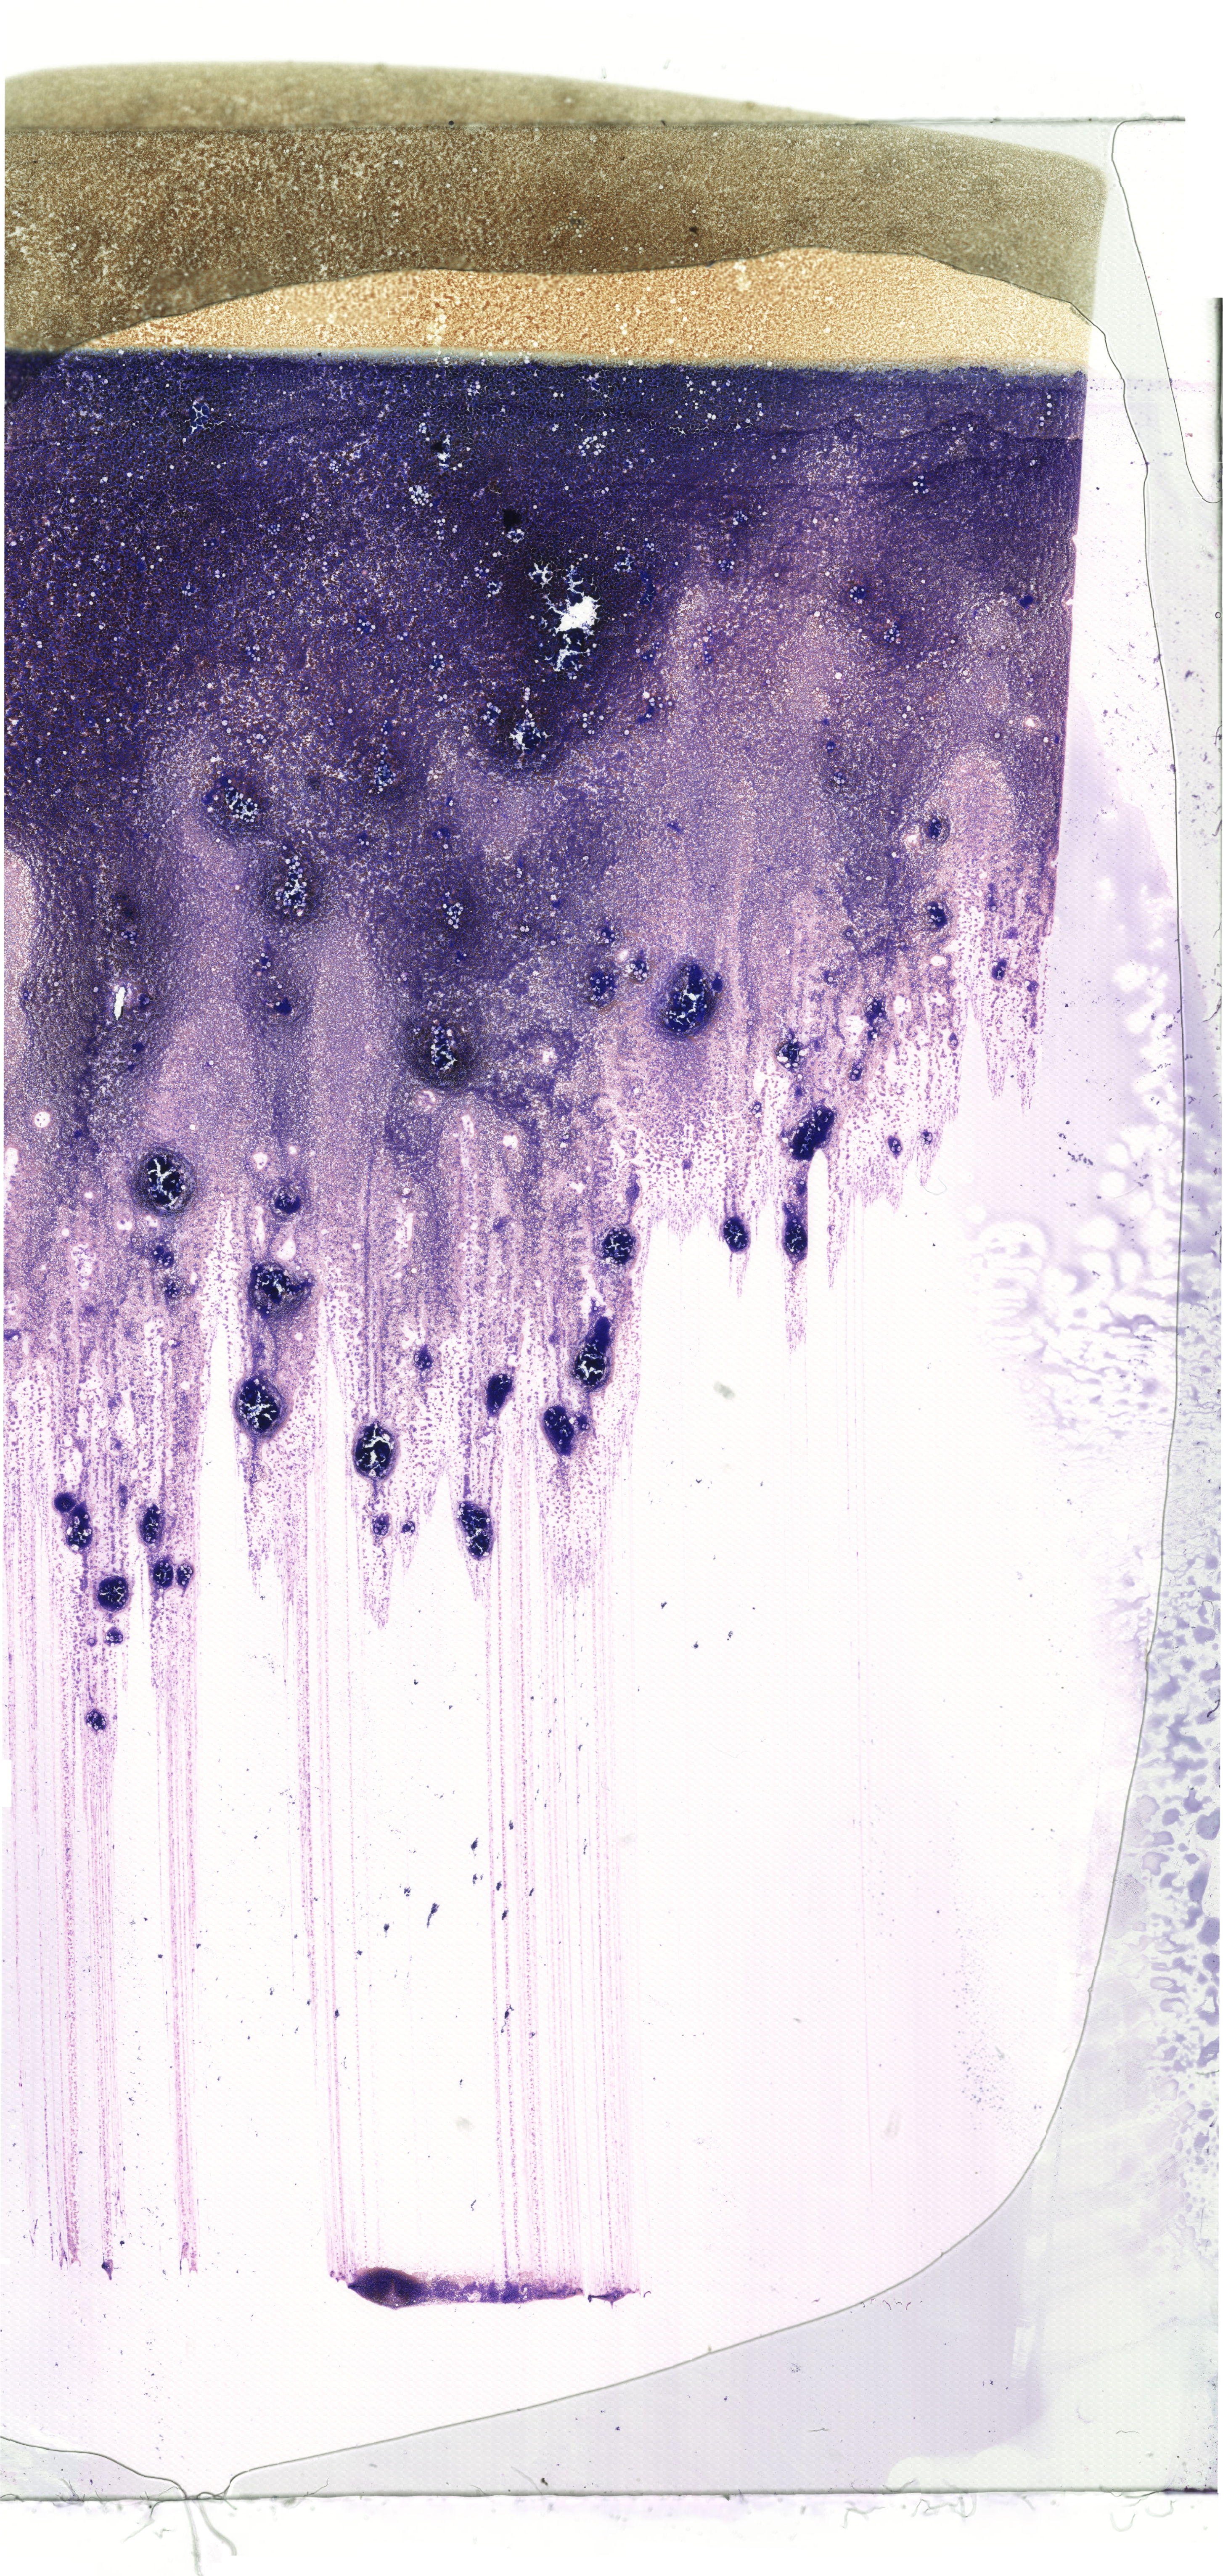
Bone marrow aspirate smear, May-Grünwald–Giemsa stain, whole-slide image, a low-resolution overview of the entire scanned area, about 20.6 x 43.4 mm. Patient sex: female.
Diagnosis: Acute Myeloid Leukemia with Maturation.